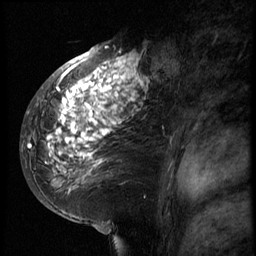
Breast MRI (dynamic contrast-enhanced), one sagittal slice. Slice 41 of 66 in the series (ordered by position). 3 images stored at this slice position (order not interpretable as contrast timing). 1.5 T. TE 4.2 ms, TR 8.9 ms. 2.5 mm slice thickness. 256 × 256 image matrix, field of view 200 × 200 mm. Female patient, age 39 years. Case-level facts recorded for this patient, not image findings: setting: breast cancer imaged before/during neoadjuvant chemotherapy; receptor status: HER2-positive.
Outlined on this slice (semi-automatically segmented with operator editing):
- analysis volume of interest (the breast-tissue region the enhancement analysis was run in; not a lesion): bounding box [x1, y1, x2, y2] px = [29, 44, 166, 196]
- tumour enhancement mask (voxels above the 140 % enhancement threshold inside the analysis volume of interest): [29, 46, 149, 182]